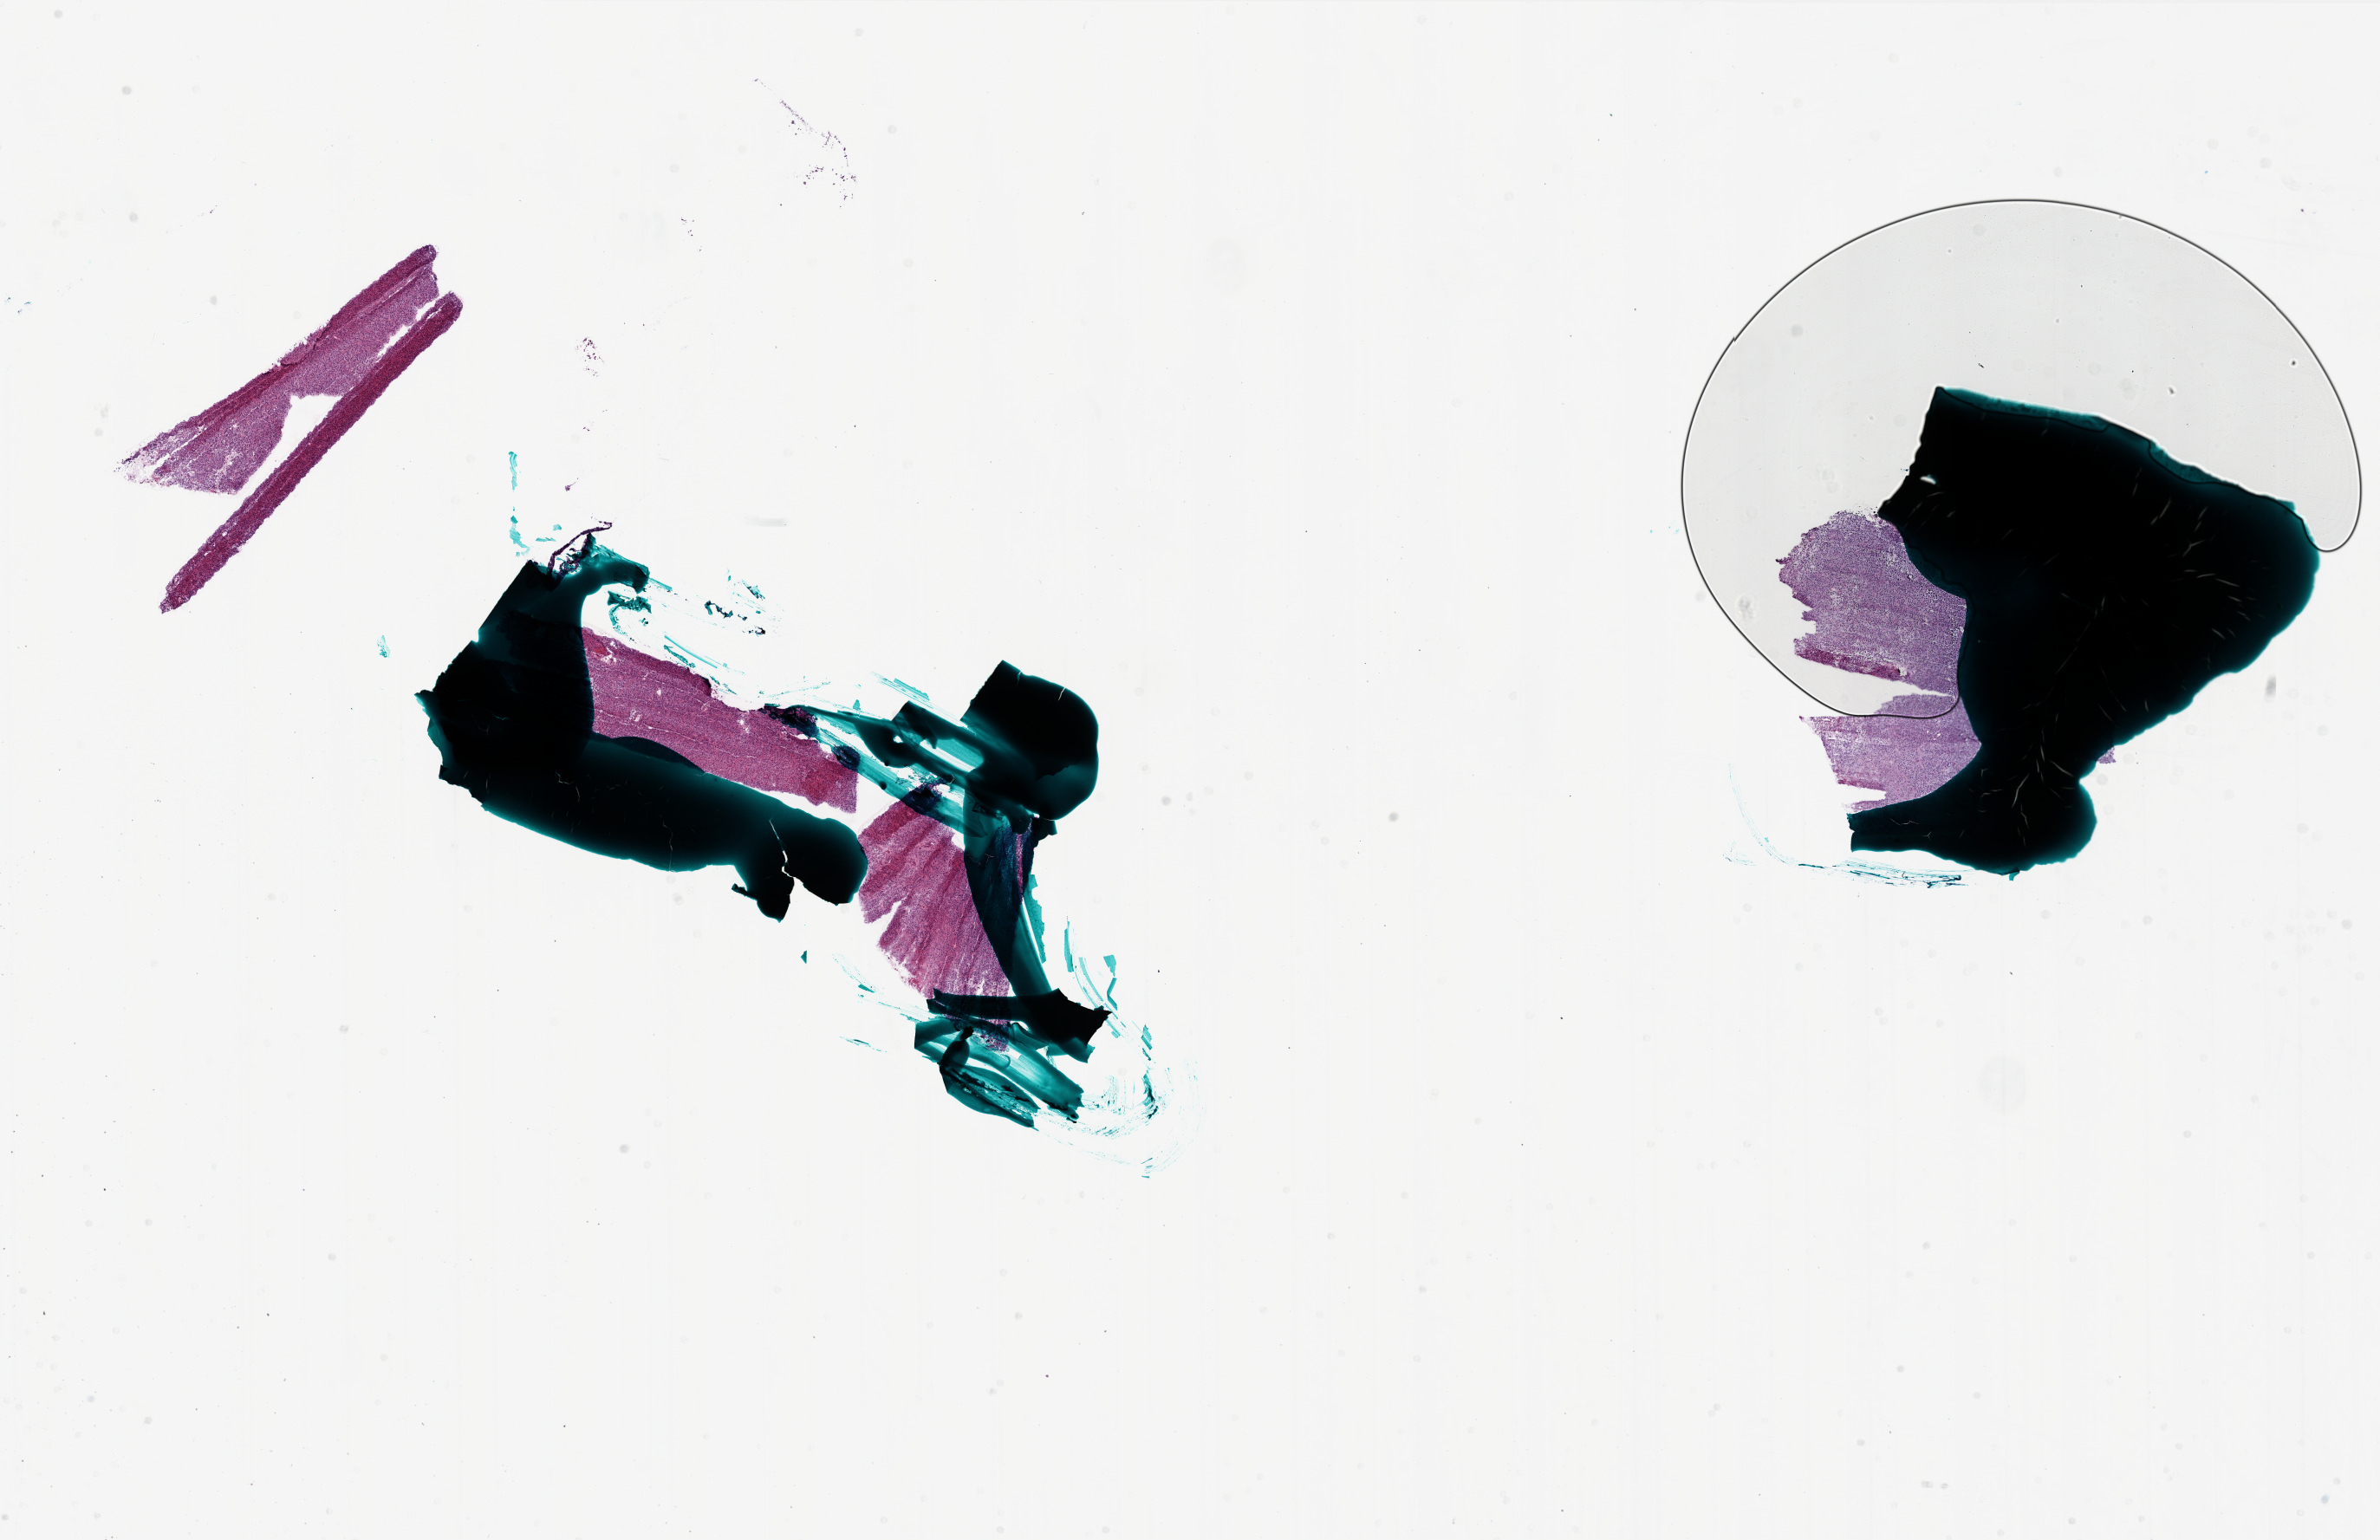
H&E whole-slide image, a low-resolution overview of the entire scanned area, about 22.0 x 14.2 mm (slide scanned at 20x). Frozen section from the bottom of the tissue portion. Brain, primary tumour sample. Male, age 47 years at initial diagnosis. Pathologist review of this section (percent, as recorded): tumour cells 90%, tumour nuclei 95%, normal cells 0%, stromal cells 10%, necrosis 0%.
Diagnosis: Glioblastoma.